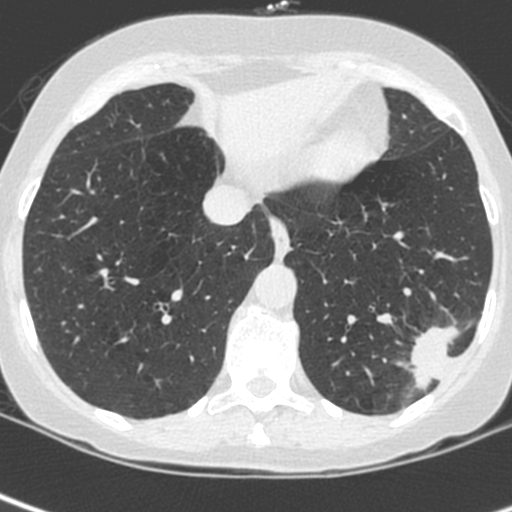
Chest CT (low-dose screening protocol), one axial image; first (baseline) screen; lung window (W 1500 / L -600 HU); 1.3 mm slice thickness; standard (soft-tissue) reconstruction kernel (C); 120 kVp; slice 171 of 252 in the series. Female, age 56 years at enrolment. Current smoker at enrolment.
- Lesion marked by an expert reader, bounding box [x1, y1, x2, y2] px = [406, 318, 476, 388].
- Screening reader's record for this exam (one nodule recorded; not confirmed to be the boxed lesion): non-calcified nodule or mass ≥4 mm, left lower lobe, 37 × 29 mm, spiculated (stellate) margins, ground glass attenuation.
- Participant outcome: lung cancer diagnosed 91 days after this screen — squamous cell carcinoma, NOS, left lower lobe, poorly differentiated (G3), stage IIIA (AJCC 6th edition), 35 mm at pathology.